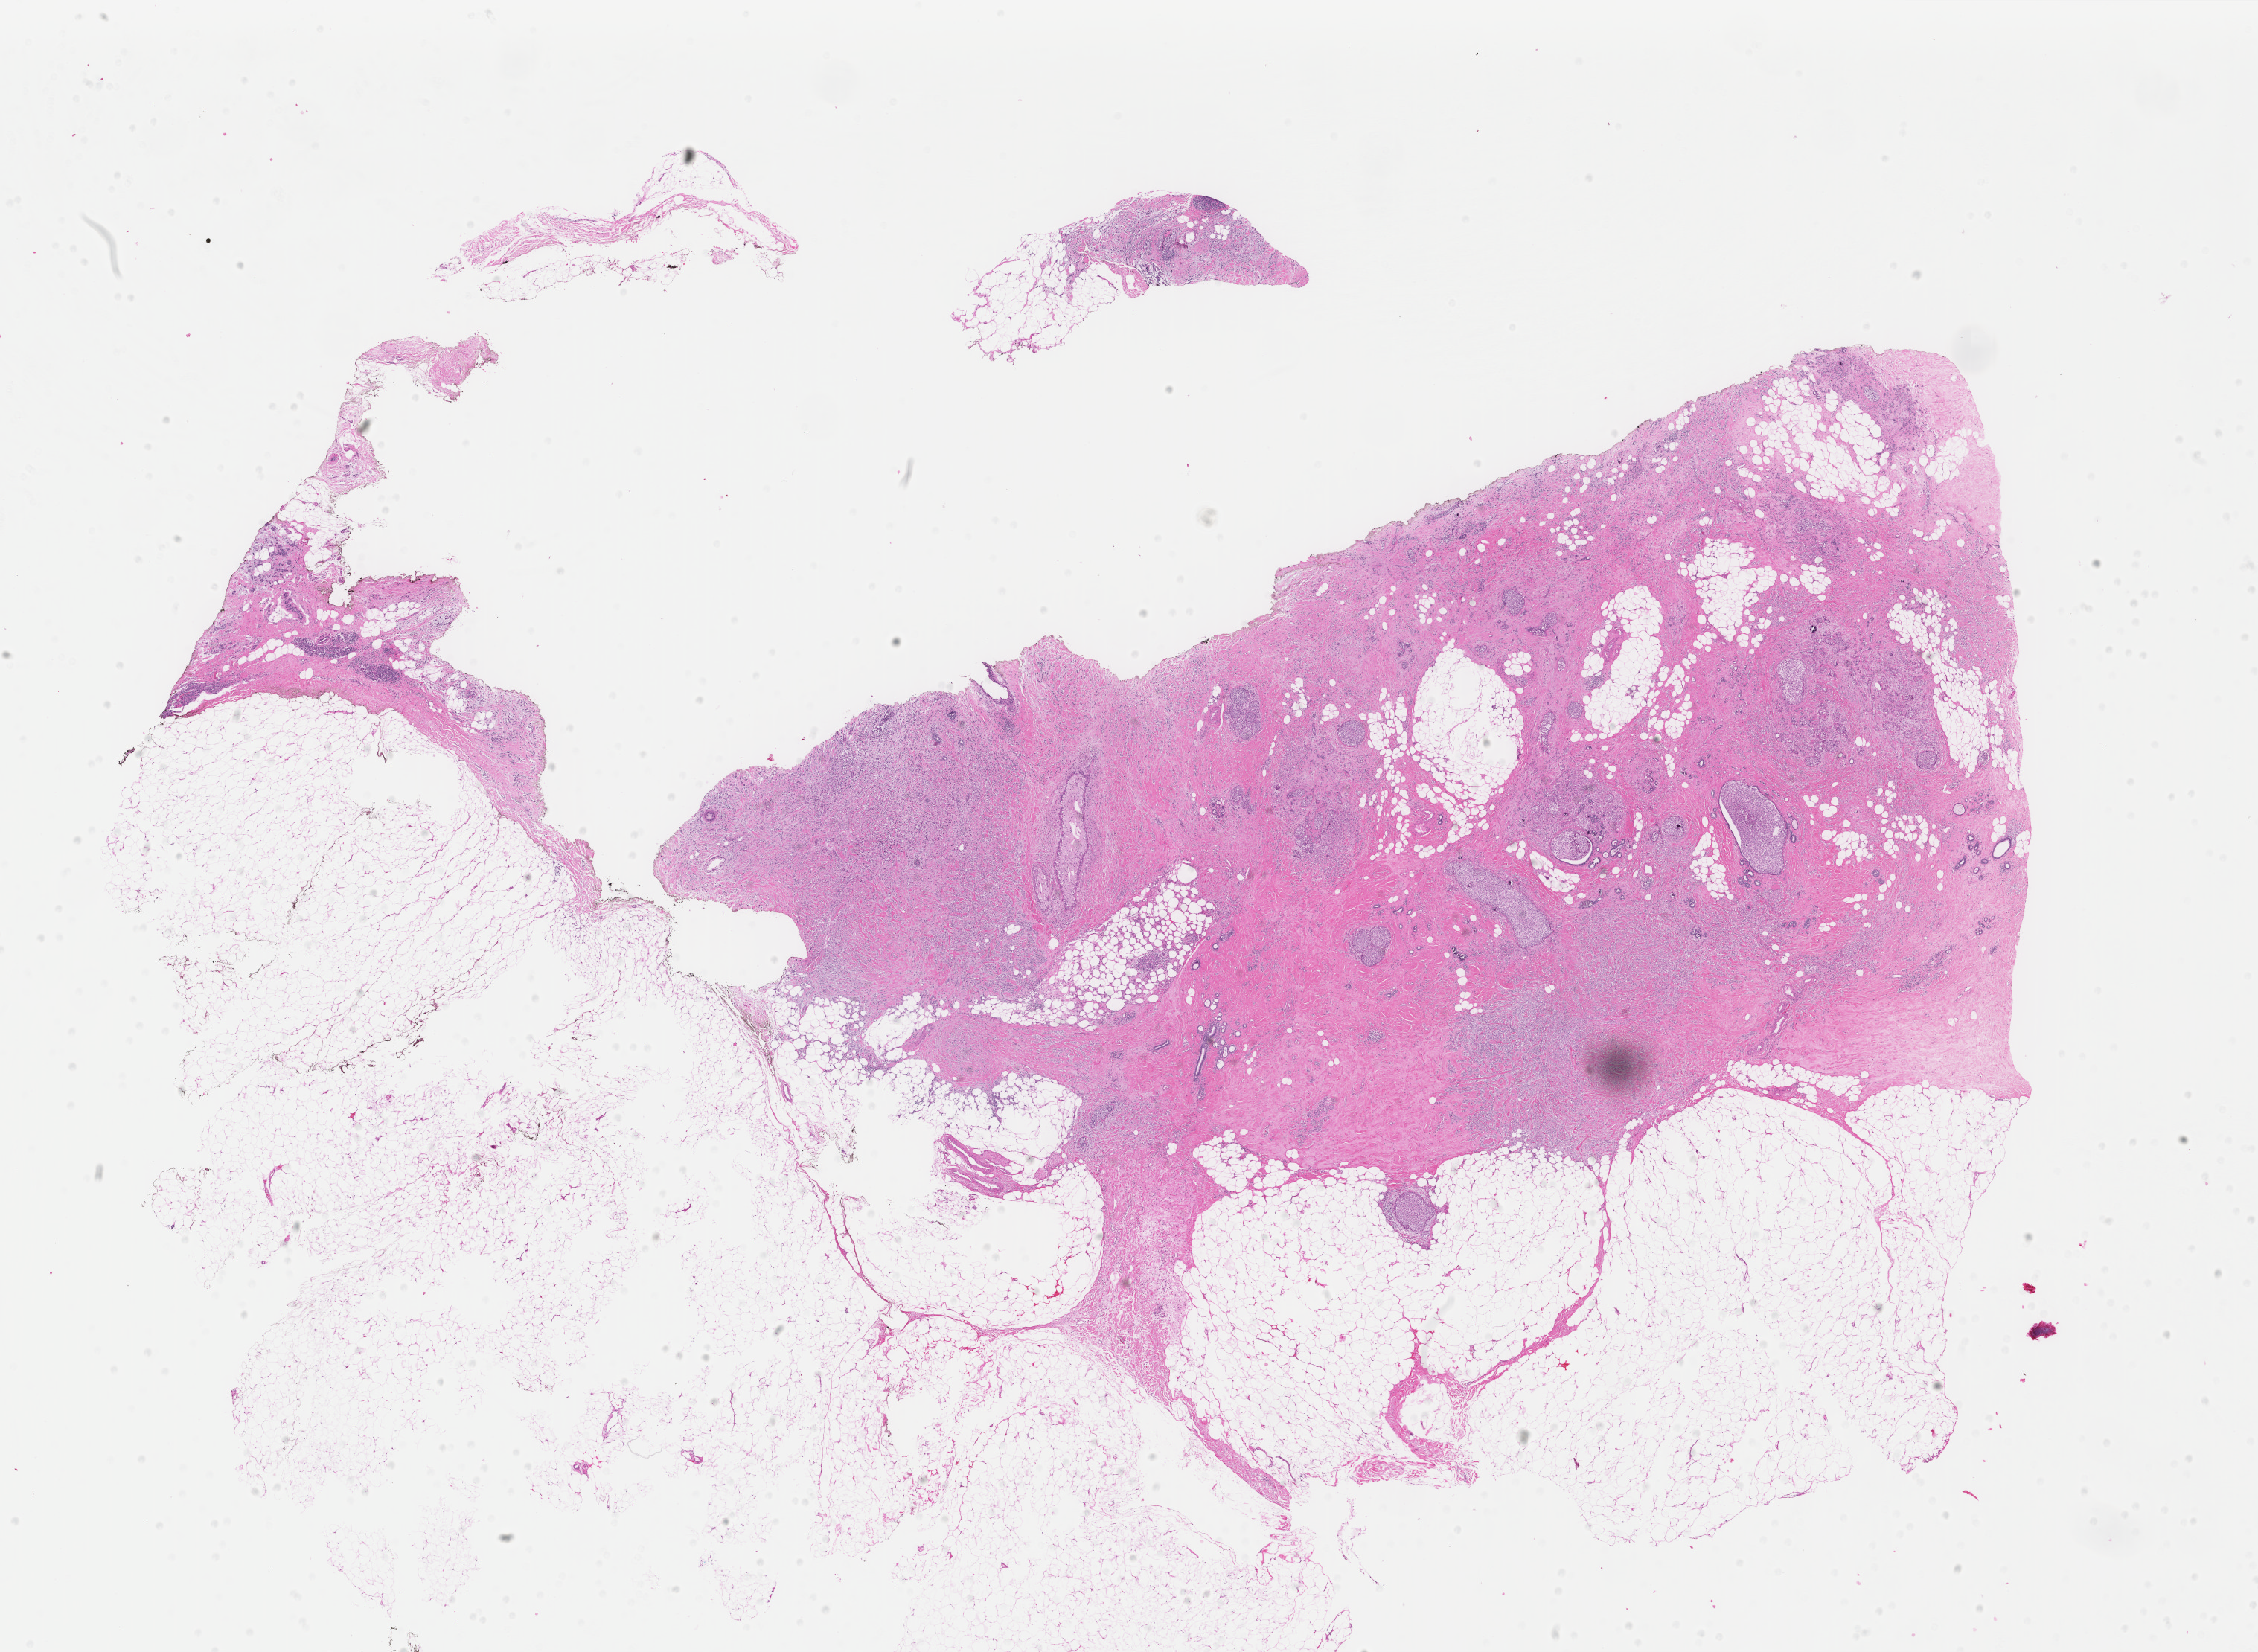
Whole-slide histology image, Hematoxylin and eosin (H&E) stained — whole scanned area (about 24.1 x 17.6 mm, from a 40x scan) shown as a low-resolution overview, formalin-fixed paraffin-embedded (FFPE) diagnostic section, breast, primary tumour sample. Female, age 62 years at initial diagnosis.
* lymph nodes positive (case pathology): 0 of 2 examined
* AJCC pathologic stage: IIA
* laterality: right
* diagnosis: Lobular carcinoma, NOS